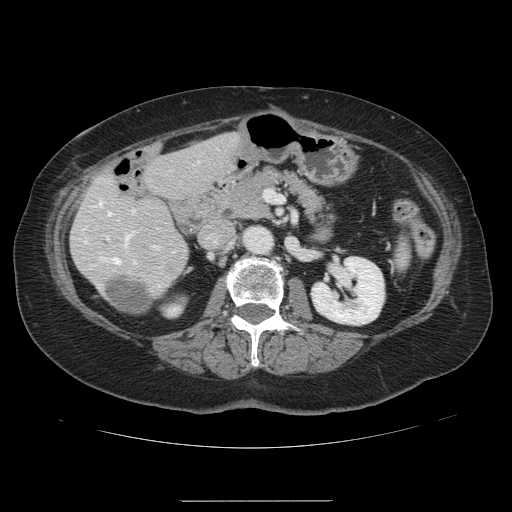
Contrast-enhanced abdominal CT, one axial slice. 120 kVp. Intravenous contrast given. Soft-tissue window (W 400 / L 40 HU). 2.5 mm slice thickness. 512 × 512 image matrix. Female patient, age 74 years. Case-level facts recorded for this patient, not image findings: diagnosis: colorectal cancer liver metastases, imaged before liver resection; multiple liver metastases: yes; largest metastasis: 7 cm.
Structures marked on this image (expert manual segmentation):
- hepatic veins: bounding box [x1, y1, x2, y2] px = [99, 201, 135, 263]
- liver: [72, 134, 240, 315]
- planned liver remnant (the part of the liver to remain after resection): [85, 134, 240, 315]
- portal vein (with intrahepatic branches): [106, 209, 159, 249]
- liver metastasis: [109, 280, 154, 312]